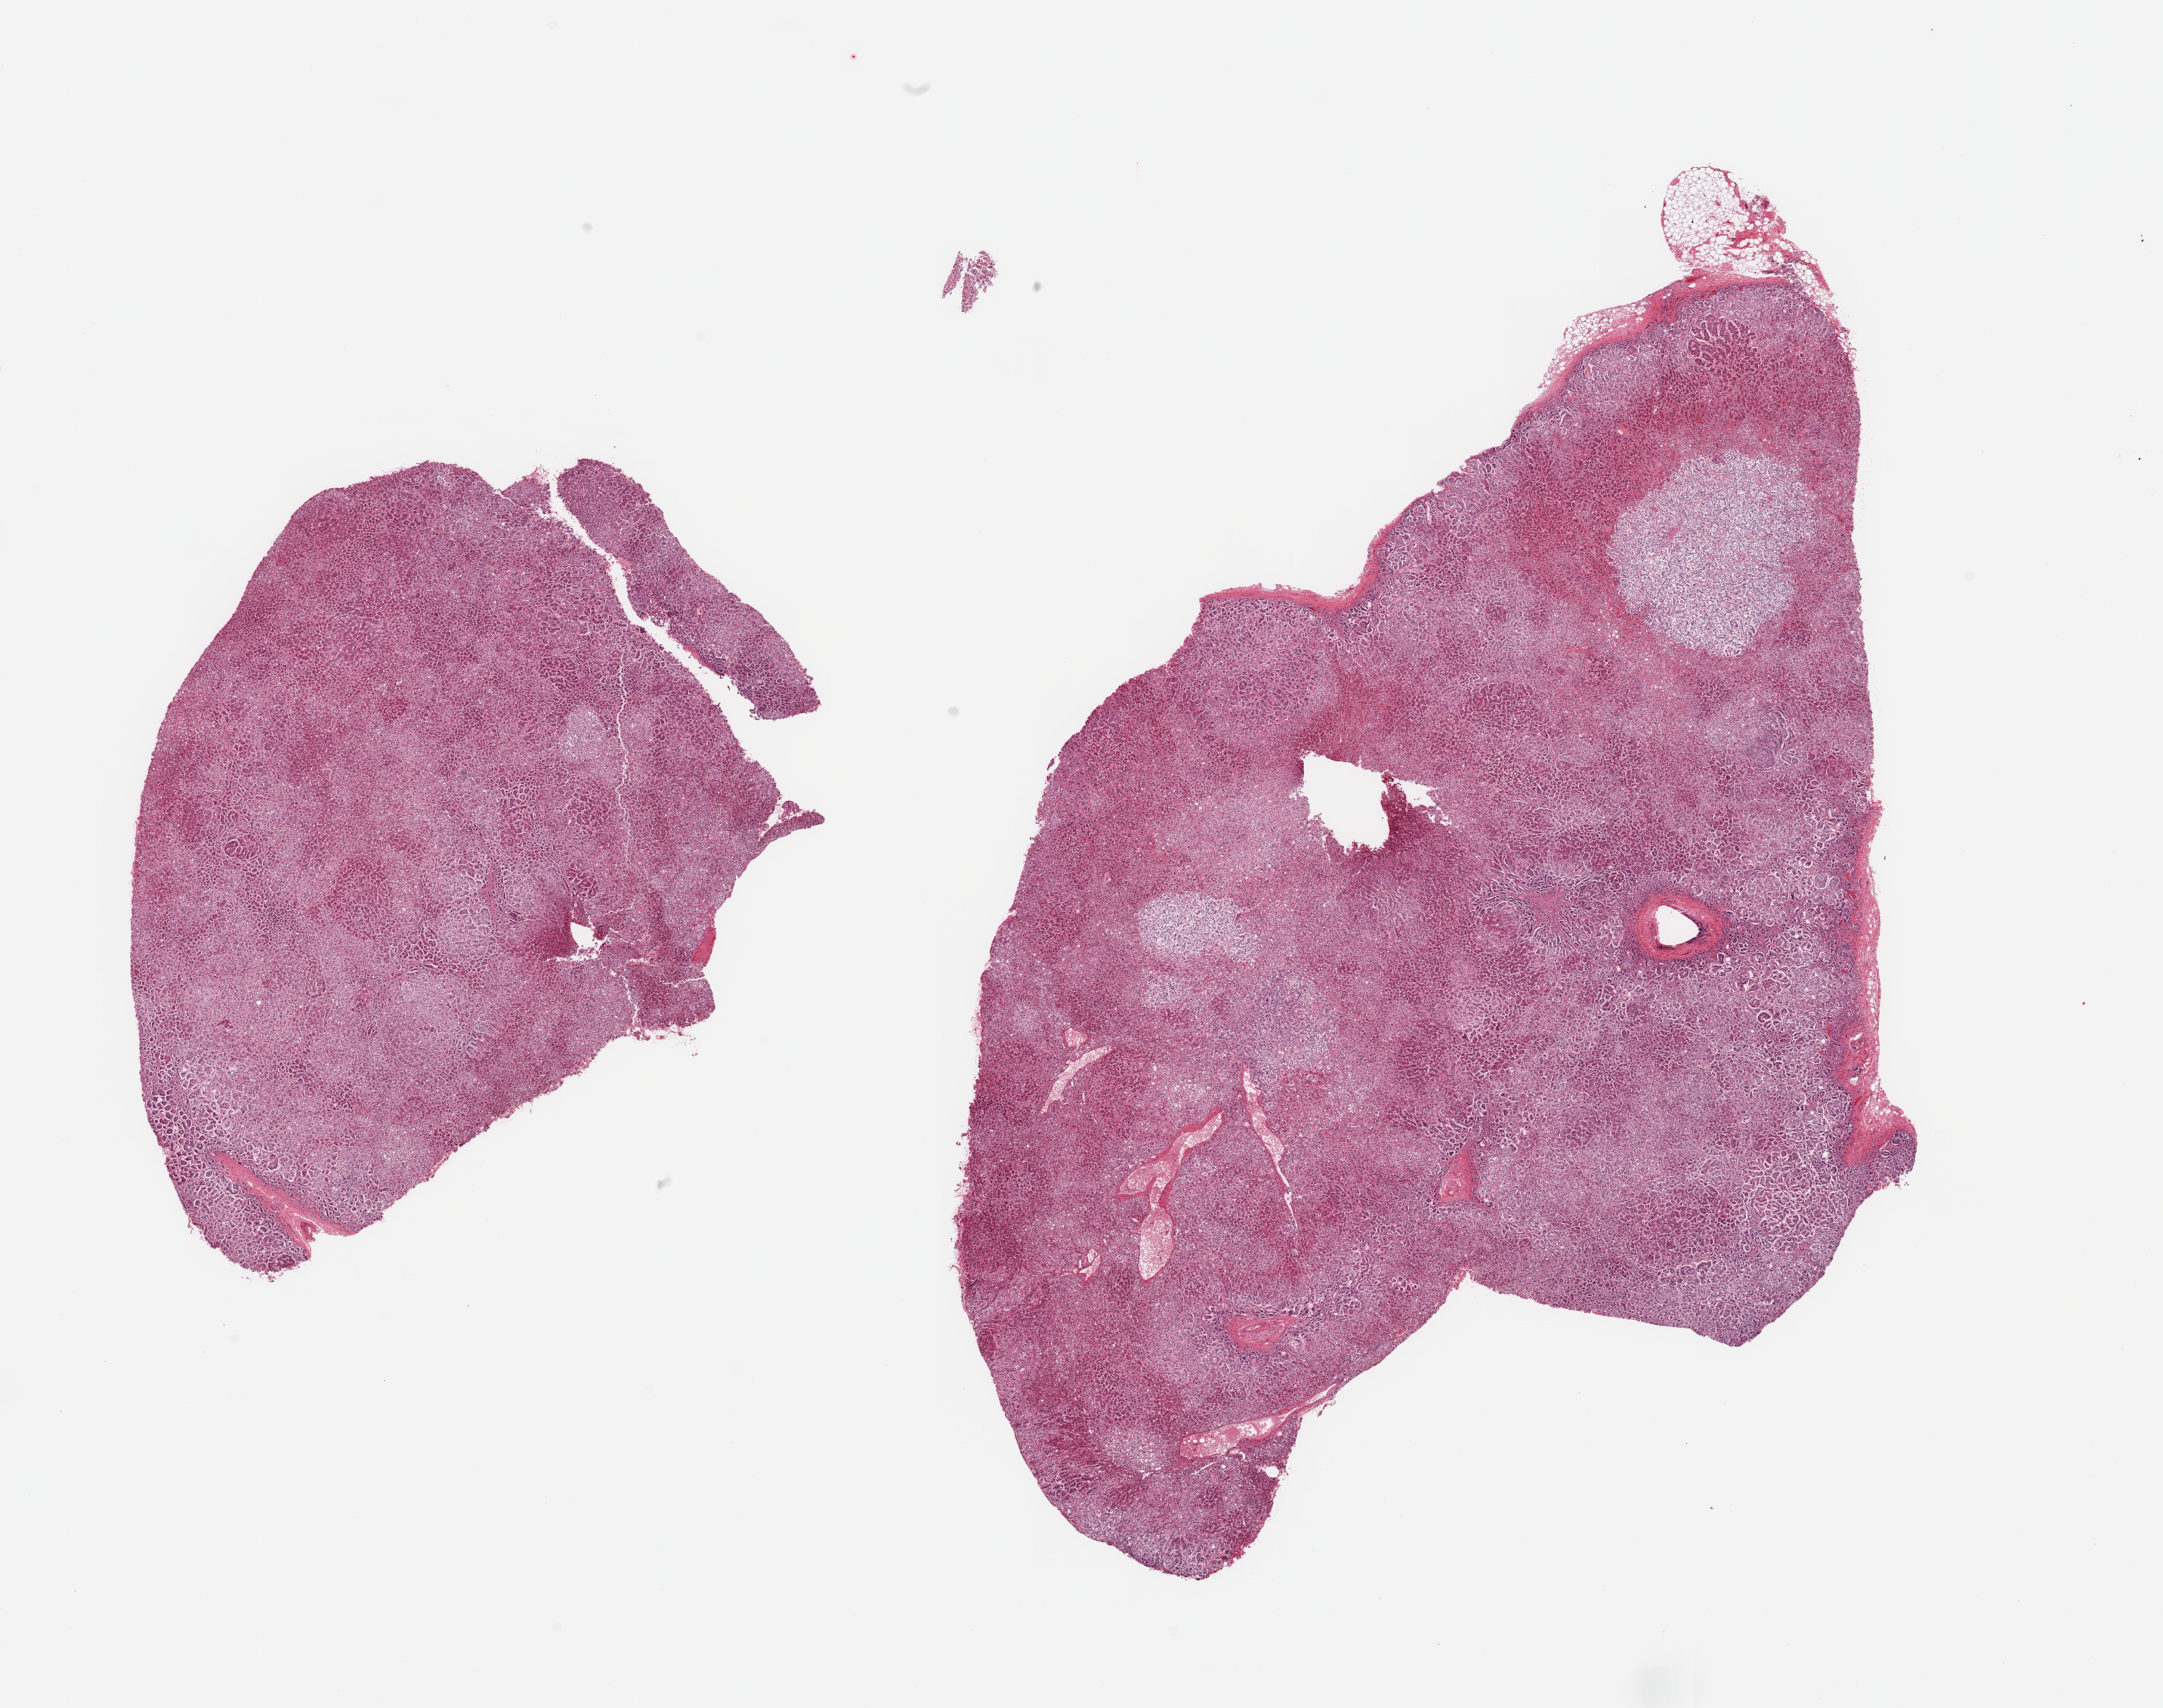
H&E whole-slide image, a low-resolution overview of the entire scanned area, about 22.6 x 17.9 mm. PAXgene-fixed paraffin-embedded (PFPE) section. Target tissue: adrenal gland. Donor tissue sample. Donor sex: male.
Reviewer comment on this tissue sample: 2 pieces; mild to moderate autolysis.